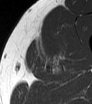
MRI of an extremity soft-tissue mass, one axial slice. Position 44 of 62 along the scan axis. MR volume resampled by the dataset authors to the PET/CT grid (not the native acquisition matrix). 92 × 104 image matrix. Male patient. Case-level facts recorded for this patient, not image findings: histological type: mixoid liposarcoma; grade: low; site of the primary tumour: left thigh.
Structures marked on this image (expert contour drawn on MRI and transferred to this co-registered scan by the dataset authors):
- gross tumour volume (mass): bounding box (x1, y1, x2, y2) in pixels: (37, 37, 63, 64)